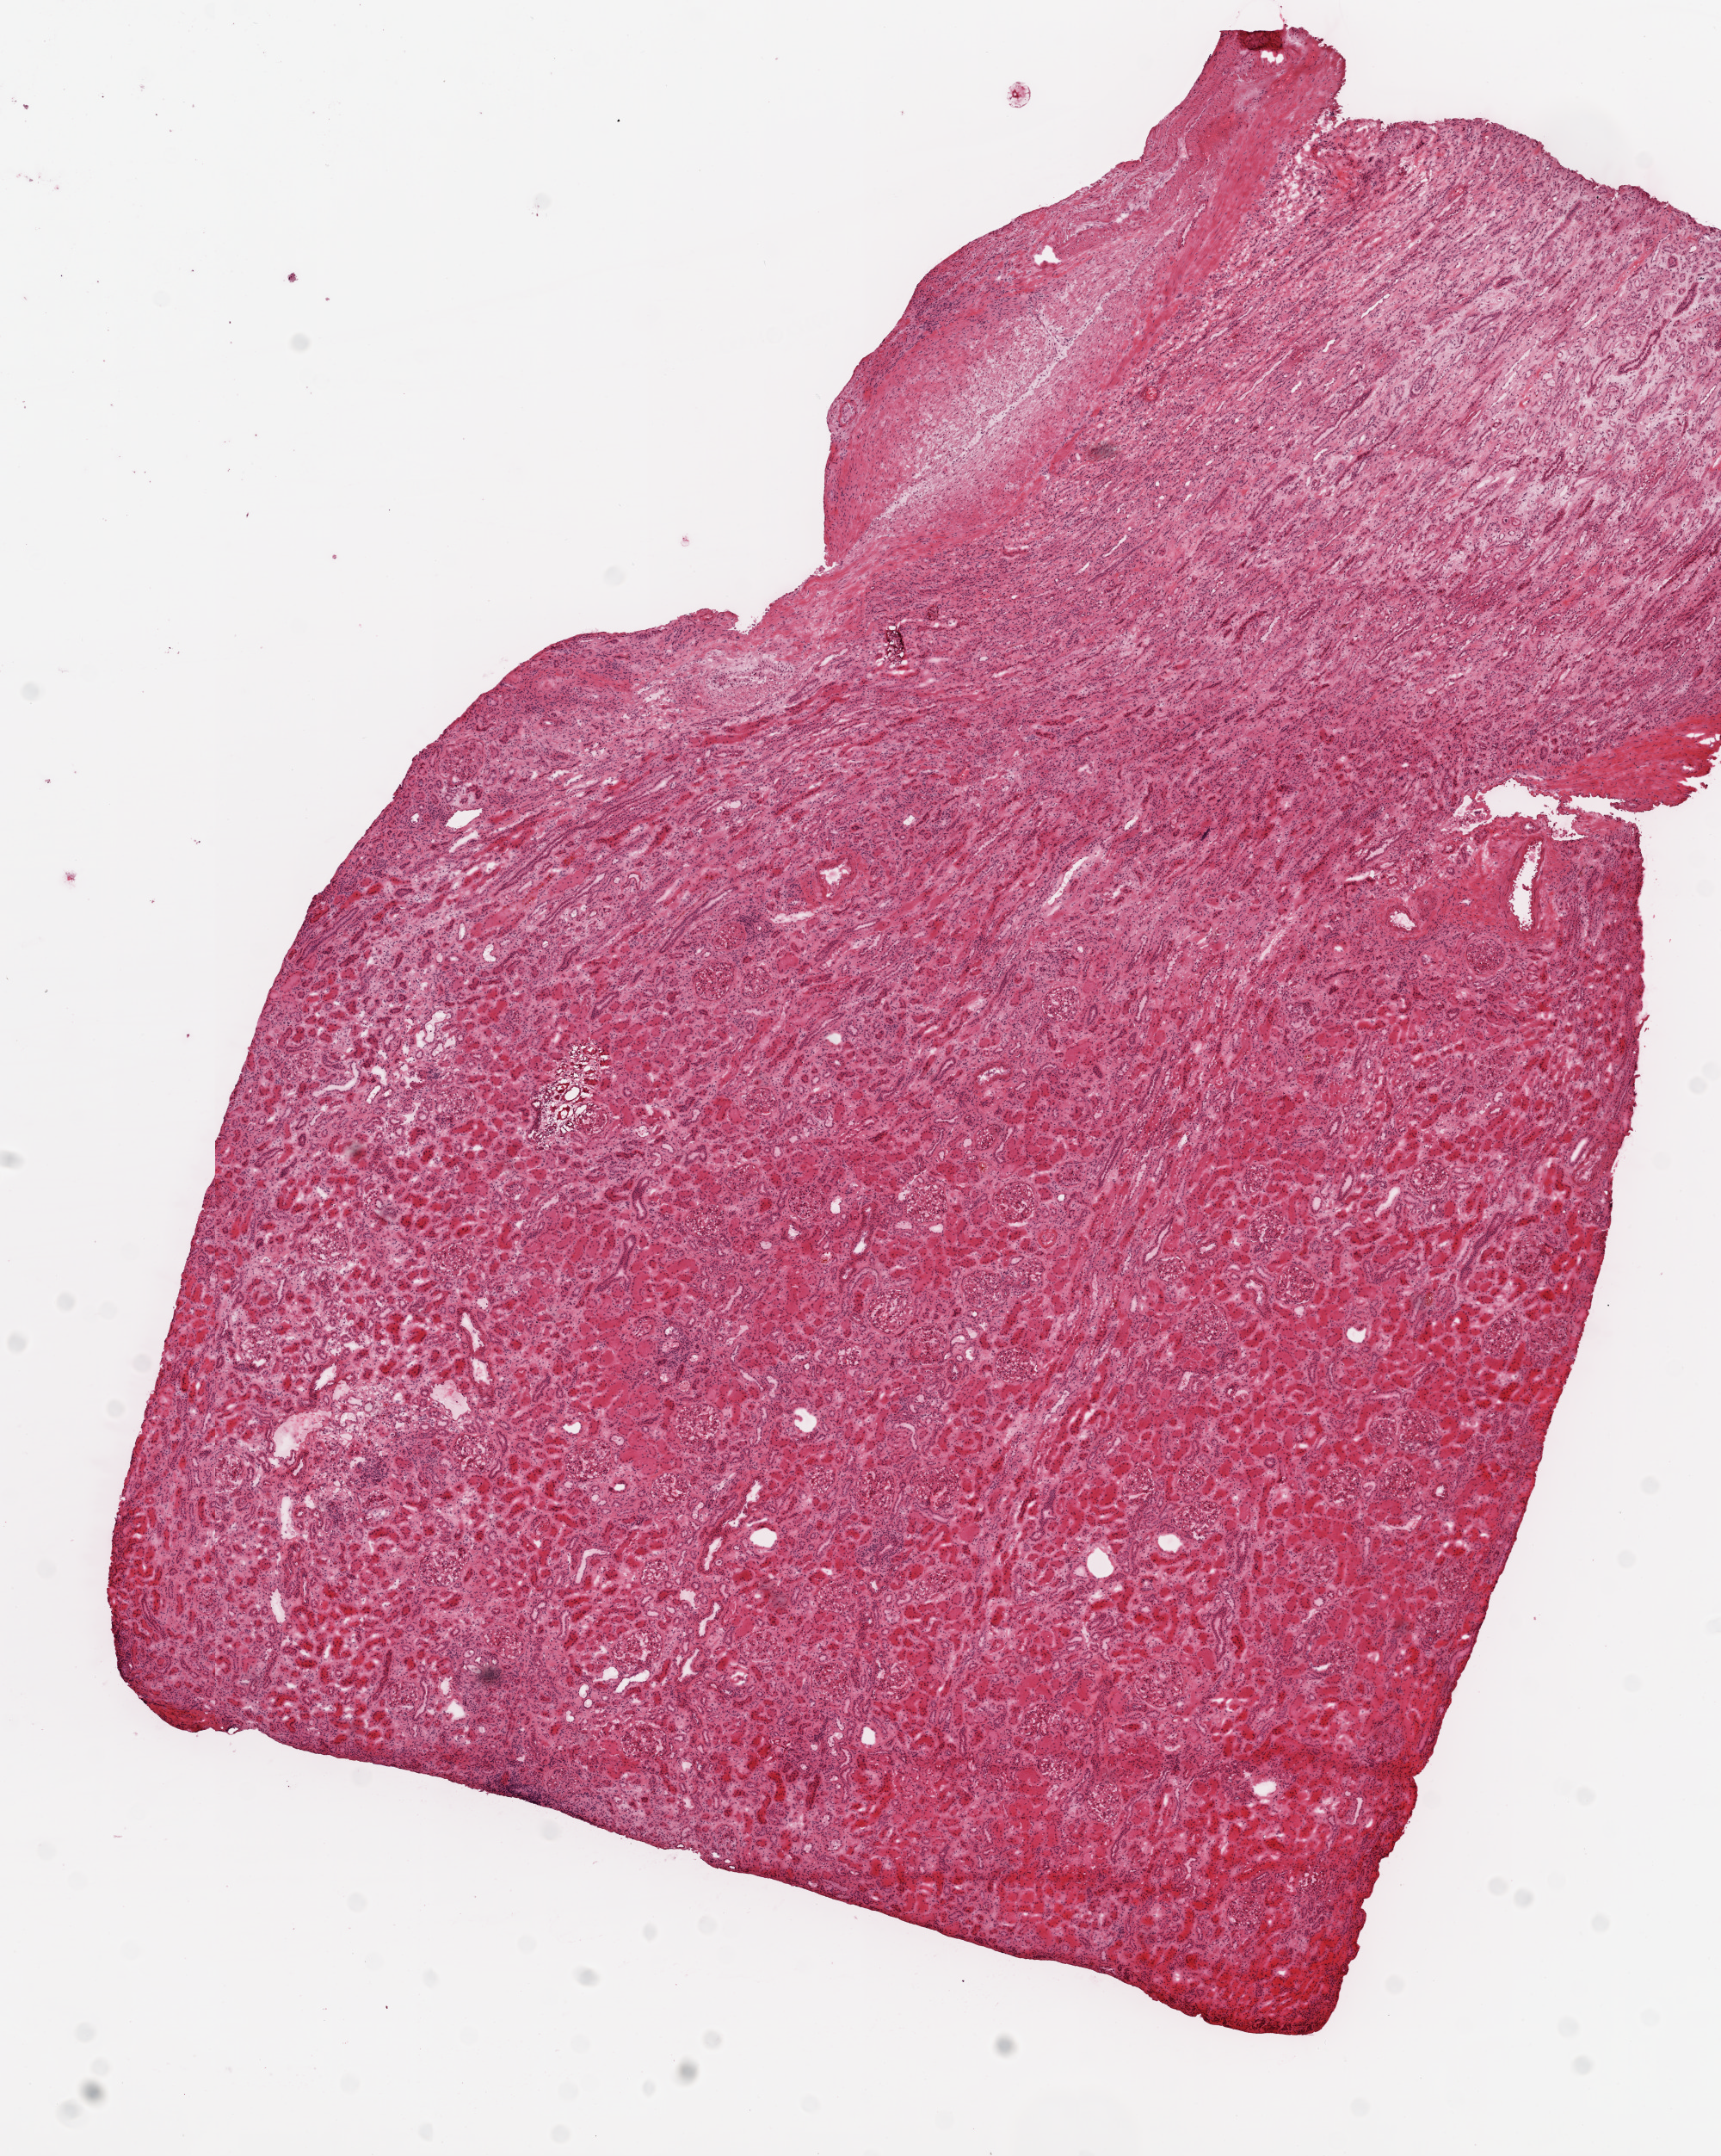
H&E-stained whole-slide image — whole scanned area (about 8.0 x 10.1 mm, acquisition: 20x scan) shown as a low-resolution overview; frozen section; kidney, solid tissue normal (non-tumour tissue) sample. Patient: male, age at initial diagnosis 40 years.
* this section: solid tissue normal sample (biorepository sample class)
* patient diagnosis: Clear cell adenocarcinoma, NOS